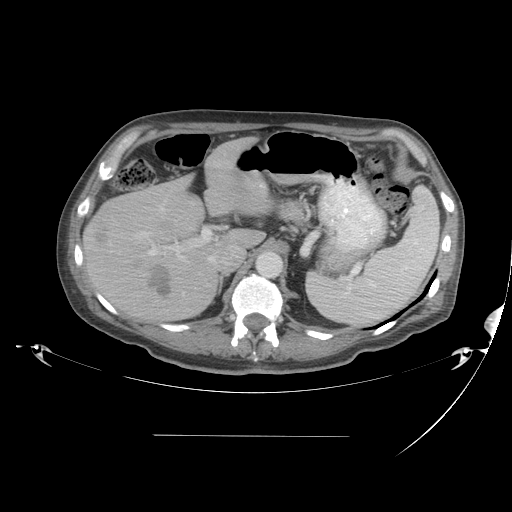
Contrast-enhanced abdominal CT, one axial slice; slice 28 of 48 in the series (ordered by position); reconstruction kernel STANDARD; intravenous contrast given; soft-tissue window (W 400 / L 40 HU); 5 mm slice thickness; 512 × 512 image matrix, field of view 486 × 486 mm. Male patient, age 65 years. From the clinical record (not read from this slice): diagnosis: colorectal cancer liver metastases, imaged before liver resection; multiple liver metastases: yes; largest metastasis: 11 cm; disease in both lobes: yes.
Annotated regions visible in this slice (expert manual segmentation):
- hepatic veins: bounding box (x1, y1, x2, y2) in pixels: (133, 212, 211, 297)
- liver: (83, 138, 271, 320)
- planned liver remnant (the part of the liver to remain after resection): (149, 138, 271, 247)
- portal vein (with intrahepatic branches): (148, 227, 219, 260)
- liver metastasis: (134, 261, 140, 267)
- liver metastasis: (146, 265, 174, 299)
- liver metastasis: (95, 229, 110, 242)